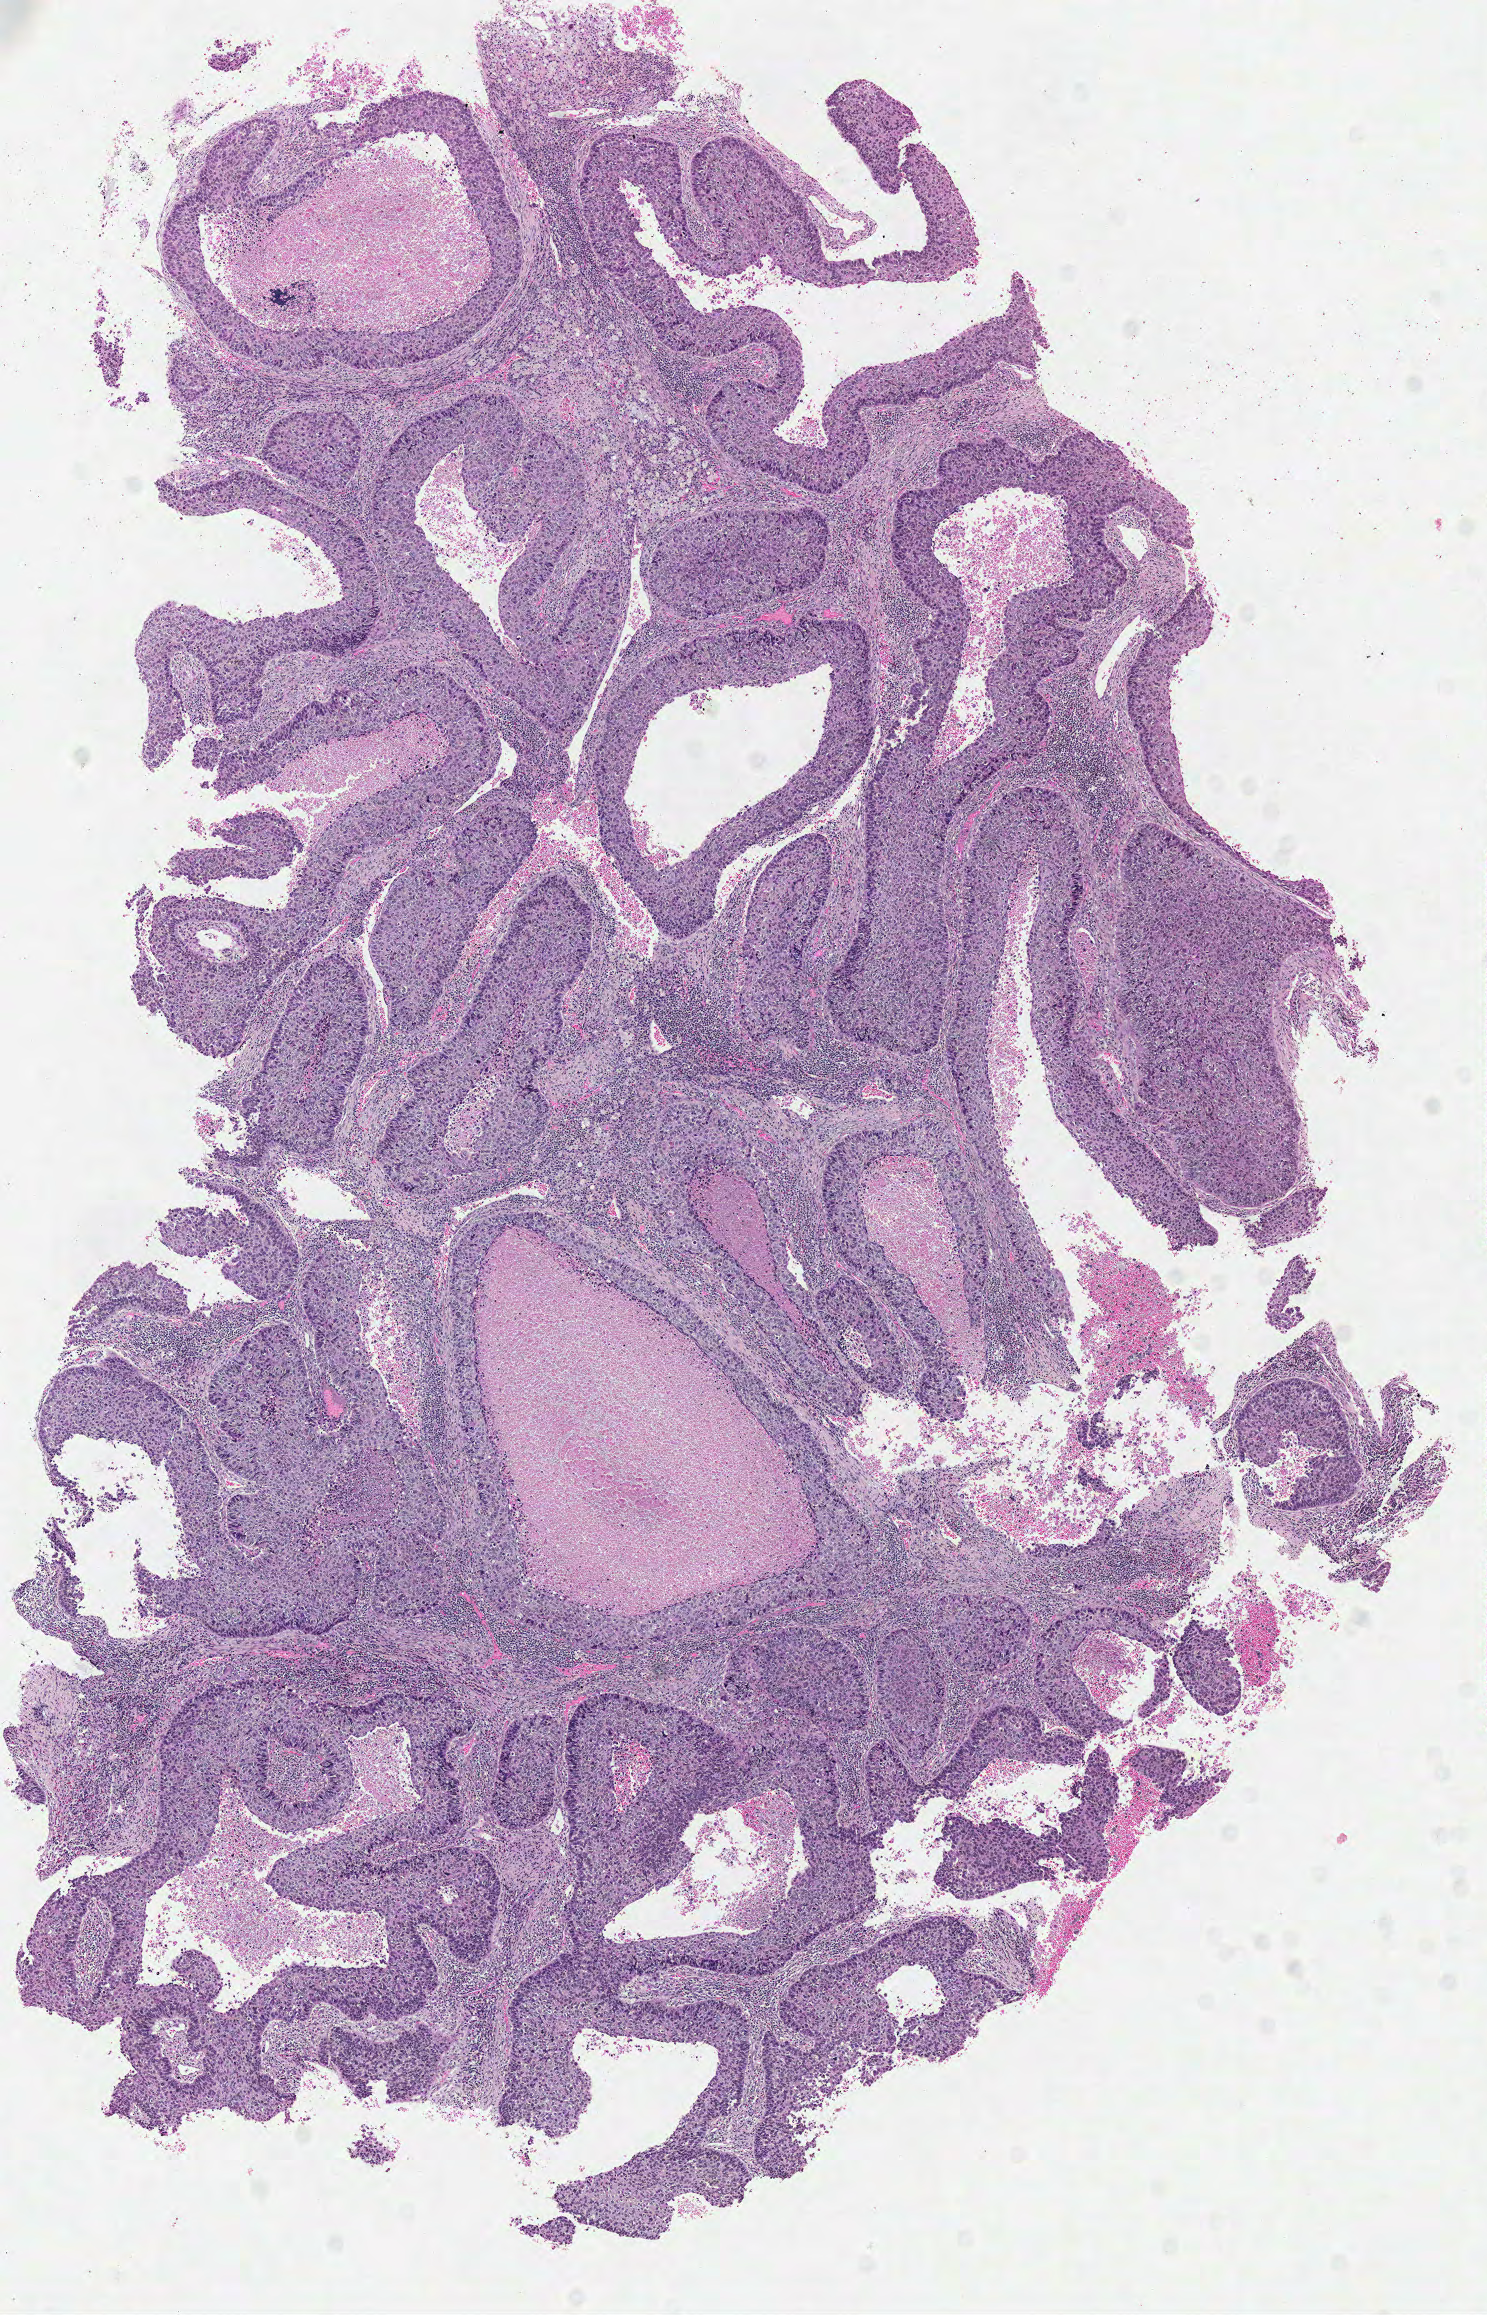
H&E whole-slide image, whole scanned area (about 5.9 x 9.1 mm, acquisition: 40x scan) shown as a low-resolution overview, formalin-fixed paraffin-embedded (FFPE) diagnostic section, primary tumour sample from the lung. Male, age 57 years at initial diagnosis.
Histologic diagnosis: Squamous cell carcinoma, NOS (upper lobe, lung).